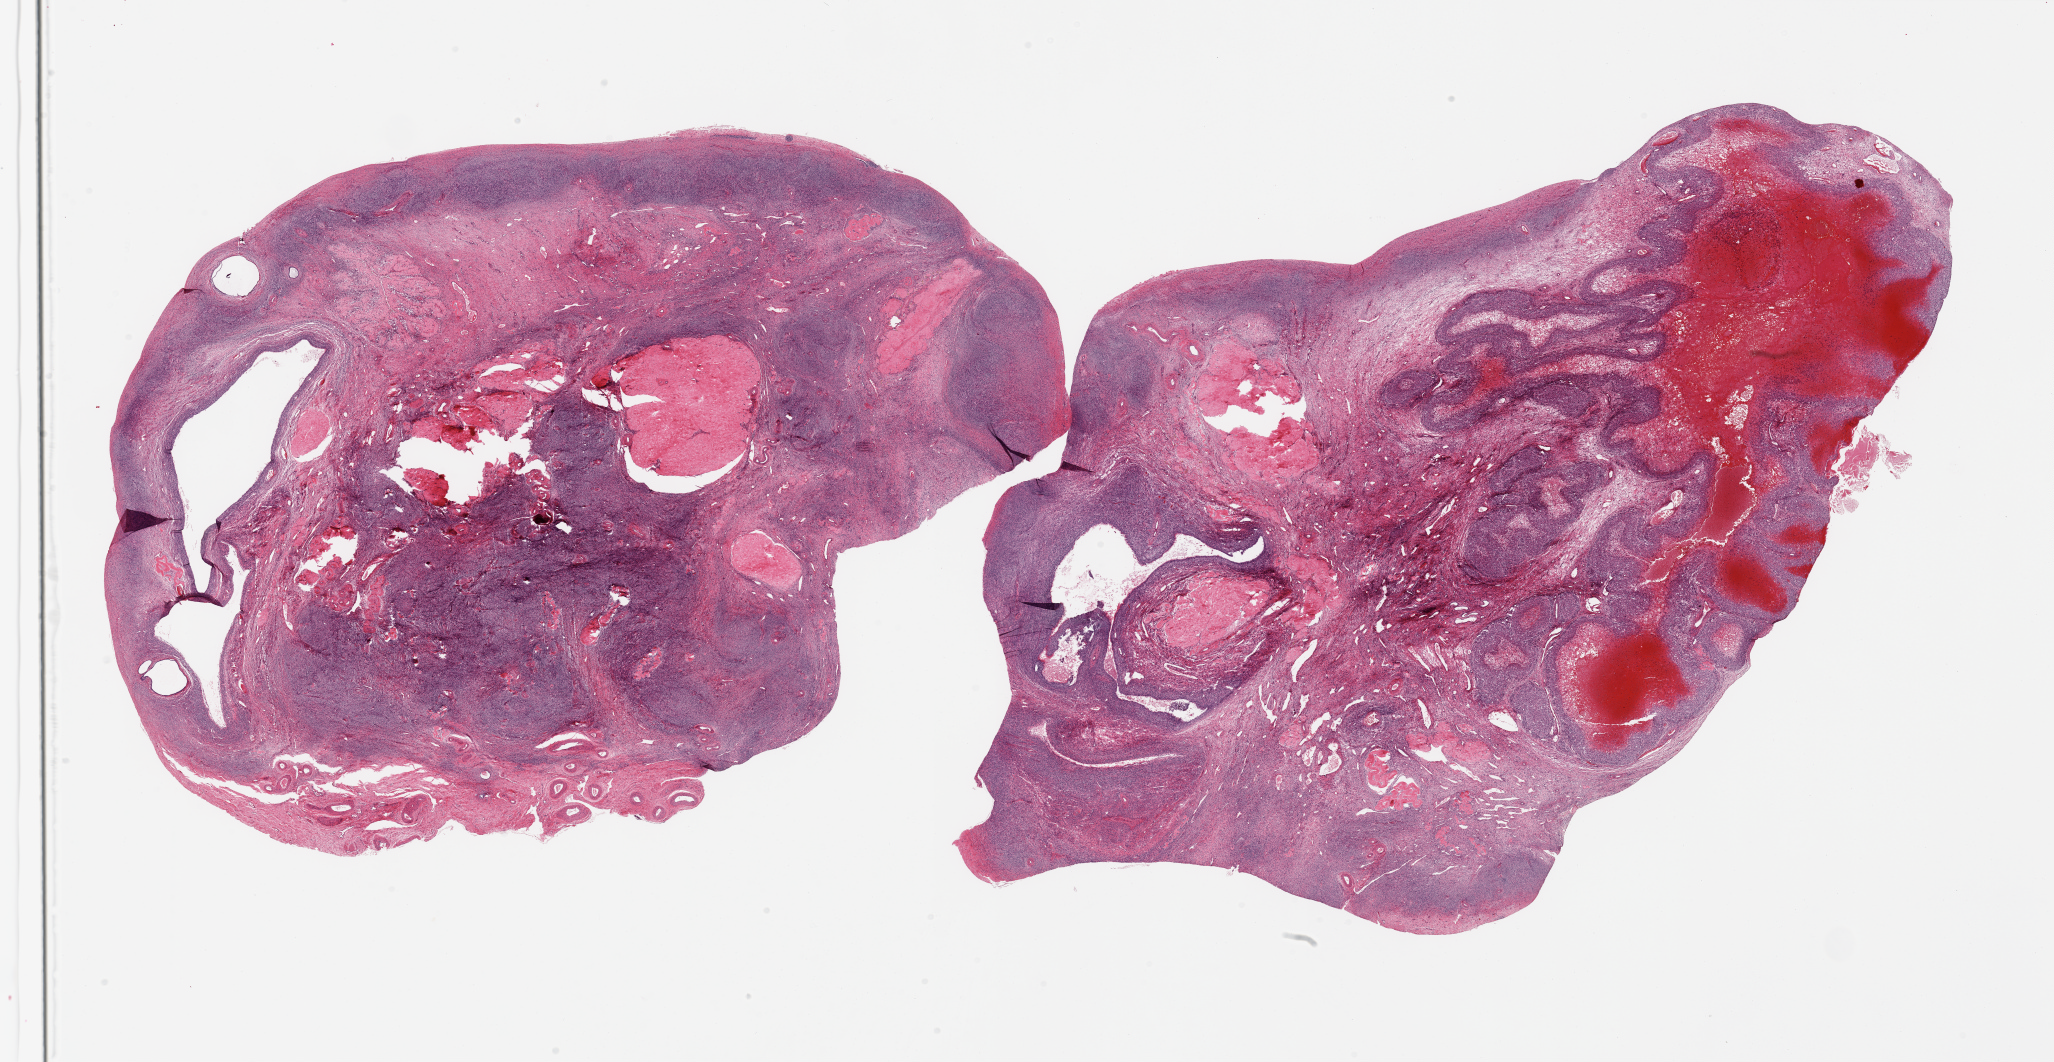
Digitized H&E-stained section — shown as a low-resolution overview of the whole scanned area (about 32.5 x 16.8 mm). PAXgene-fixed, paraffin-embedded tissue. Section of ovary (target tissue). Tissue donor sample. Donor: female.
* review note (as recorded): 2 pieces; corpora in various stages of development, largest has 4mm hemorrhage